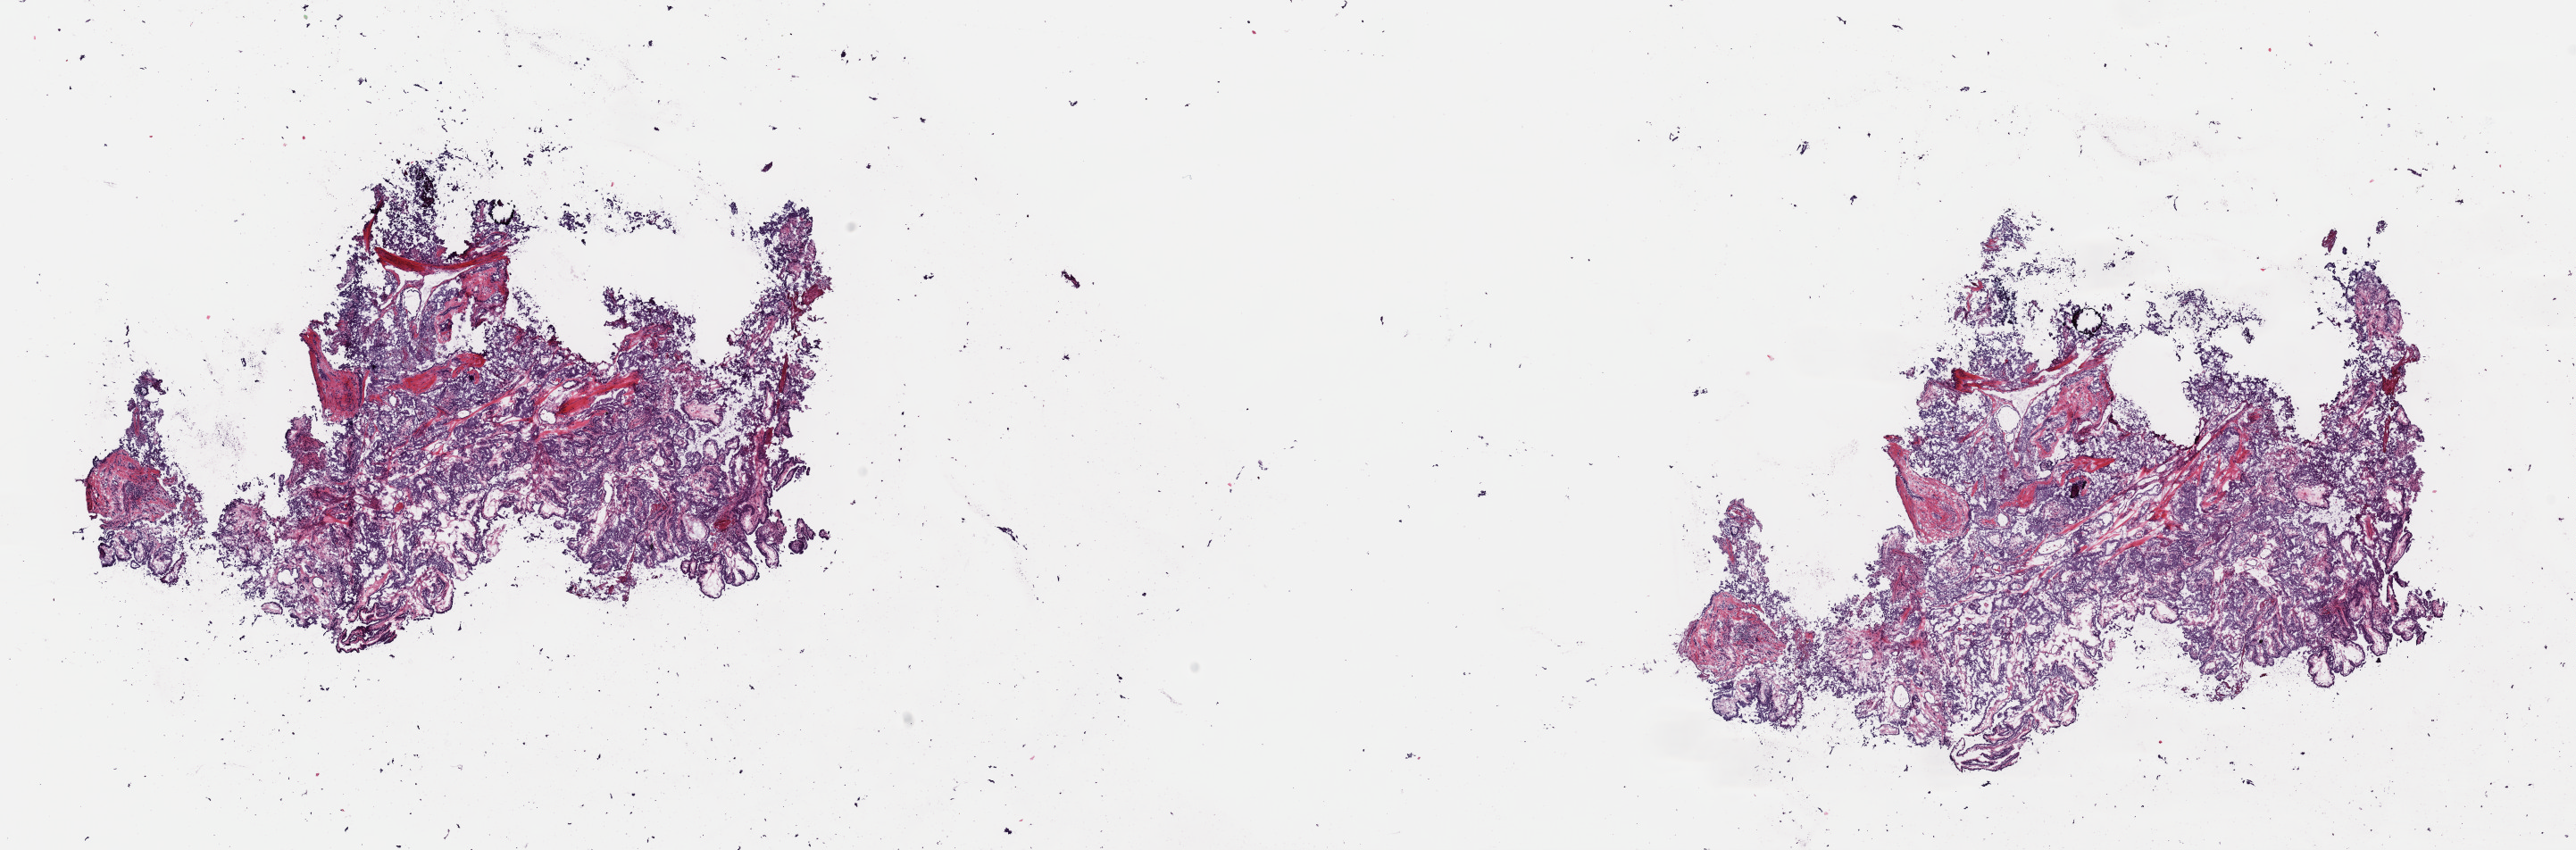
Digitized Hematoxylin and eosin (H&E) stained tissue section (whole slide), whole scanned area (about 22.8 x 7.5 mm, slide scanned at 40x) shown as a low-resolution overview. Frozen section from the top of the tissue portion. Sample: primary tumour, thyroid. Patient: female, age at initial diagnosis 27 years. Pathologist review of this section (percent, as recorded): tumour cells 98%, tumour nuclei 90%, normal cells 0%, stromal cells 2%, necrosis 0%. Inflammatory infiltration, as recorded: lymphocyte infiltration 0%, monocyte infiltration 0%, neutrophil infiltration 0%.
- lymph nodes positive (case pathology): 0 of 2 examined
- histologic diagnosis: Papillary adenocarcinoma, NOS (thyroid gland)
- laterality: right
- AJCC pathologic stage: I (6th edition)